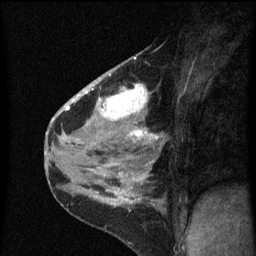
Breast MRI (dynamic contrast-enhanced), one sagittal slice; slice 38 of 60 in the series (ordered by position); dynamic contrast-enhanced series, image 2 of 3 at this slice position (ordered by acquisition); 1.5 T; TE 4.2 ms, TR 8 ms; 2 mm slice thickness; 256 × 256 image matrix, field of view 180 × 180 mm. Patient: female, 38 years.
Outlined on this slice (semi-automatic segmentation, software-assisted and operator-edited):
- analysis volume of interest (the breast-tissue region the enhancement analysis was run in; not a lesion): box from (x=80, y=54) to (x=165, y=151) px
- tumour enhancement mask (voxels above the 70 % enhancement threshold inside the analysis volume of interest): (x=80, y=58)–(x=159, y=145)